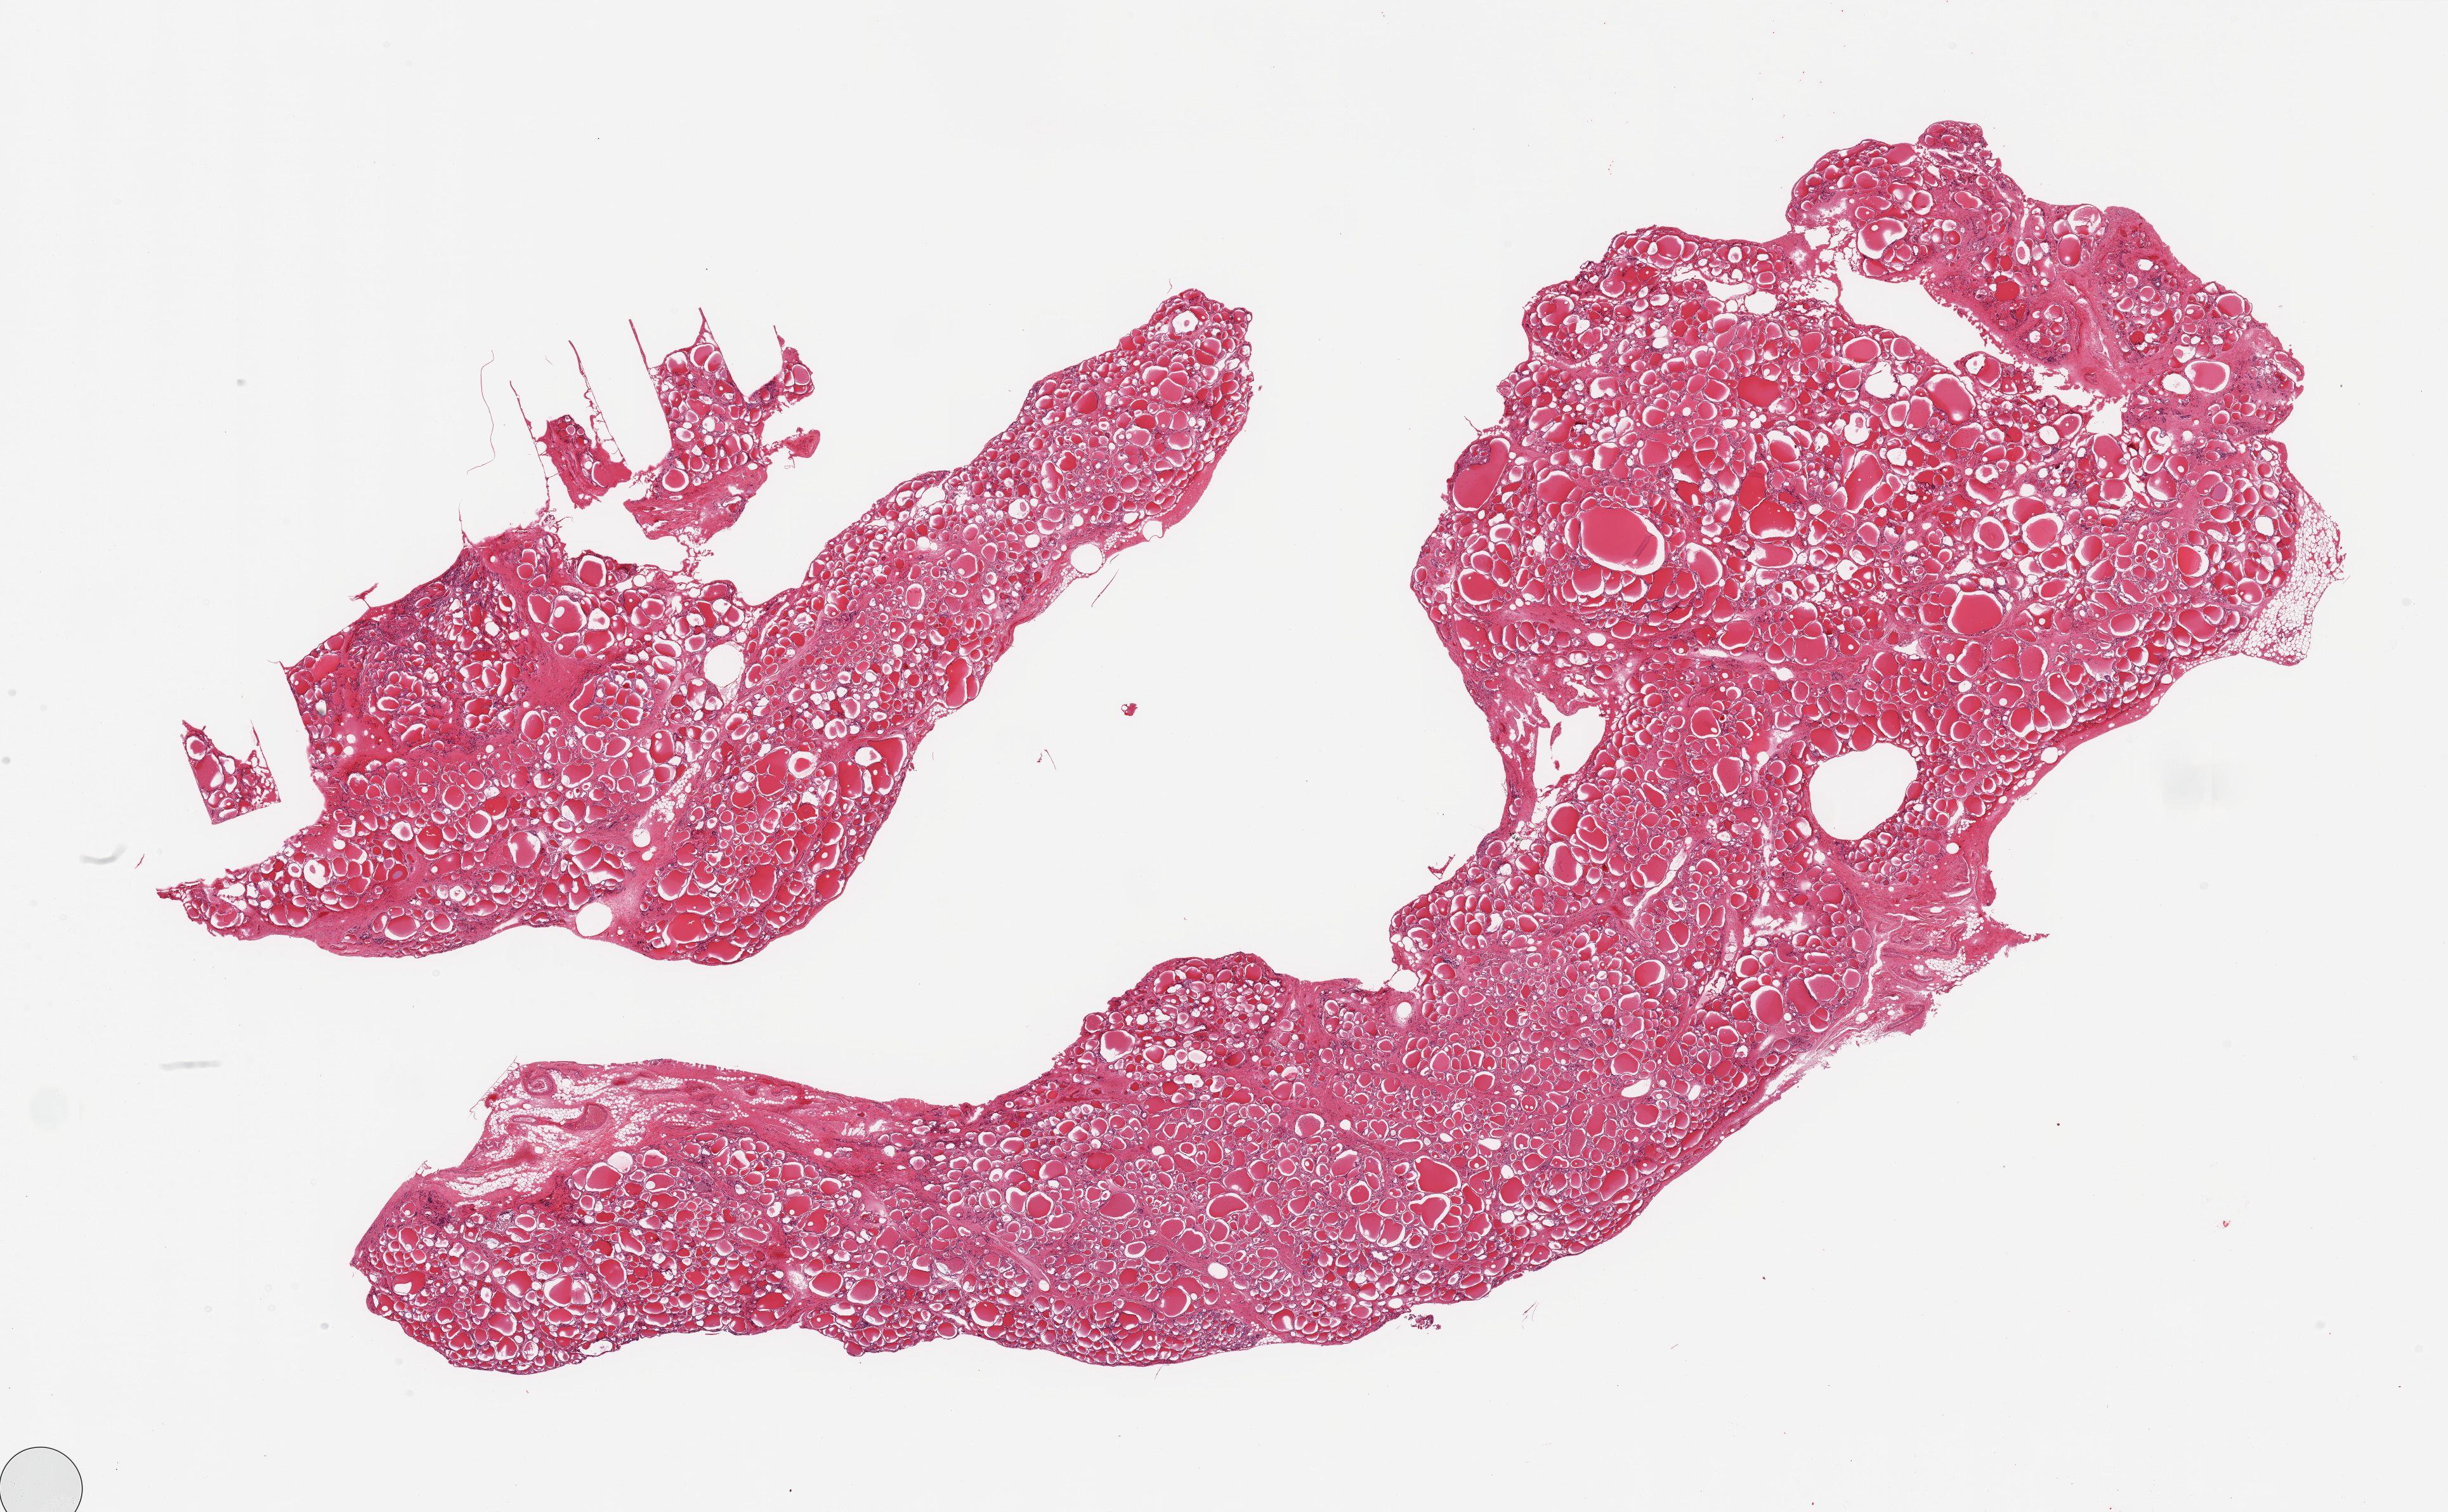
Hematoxylin and eosin (H&E) whole-slide image, brightfield, a low-resolution overview of the entire scanned area, about 30.5 x 18.9 mm, PAXgene-fixed paraffin-embedded (PFPE) section, section of thyroid (target tissue), donor tissue sample. Donor: male.
Pathologist's review note for this sample: 2 pieces, no abnormalities.